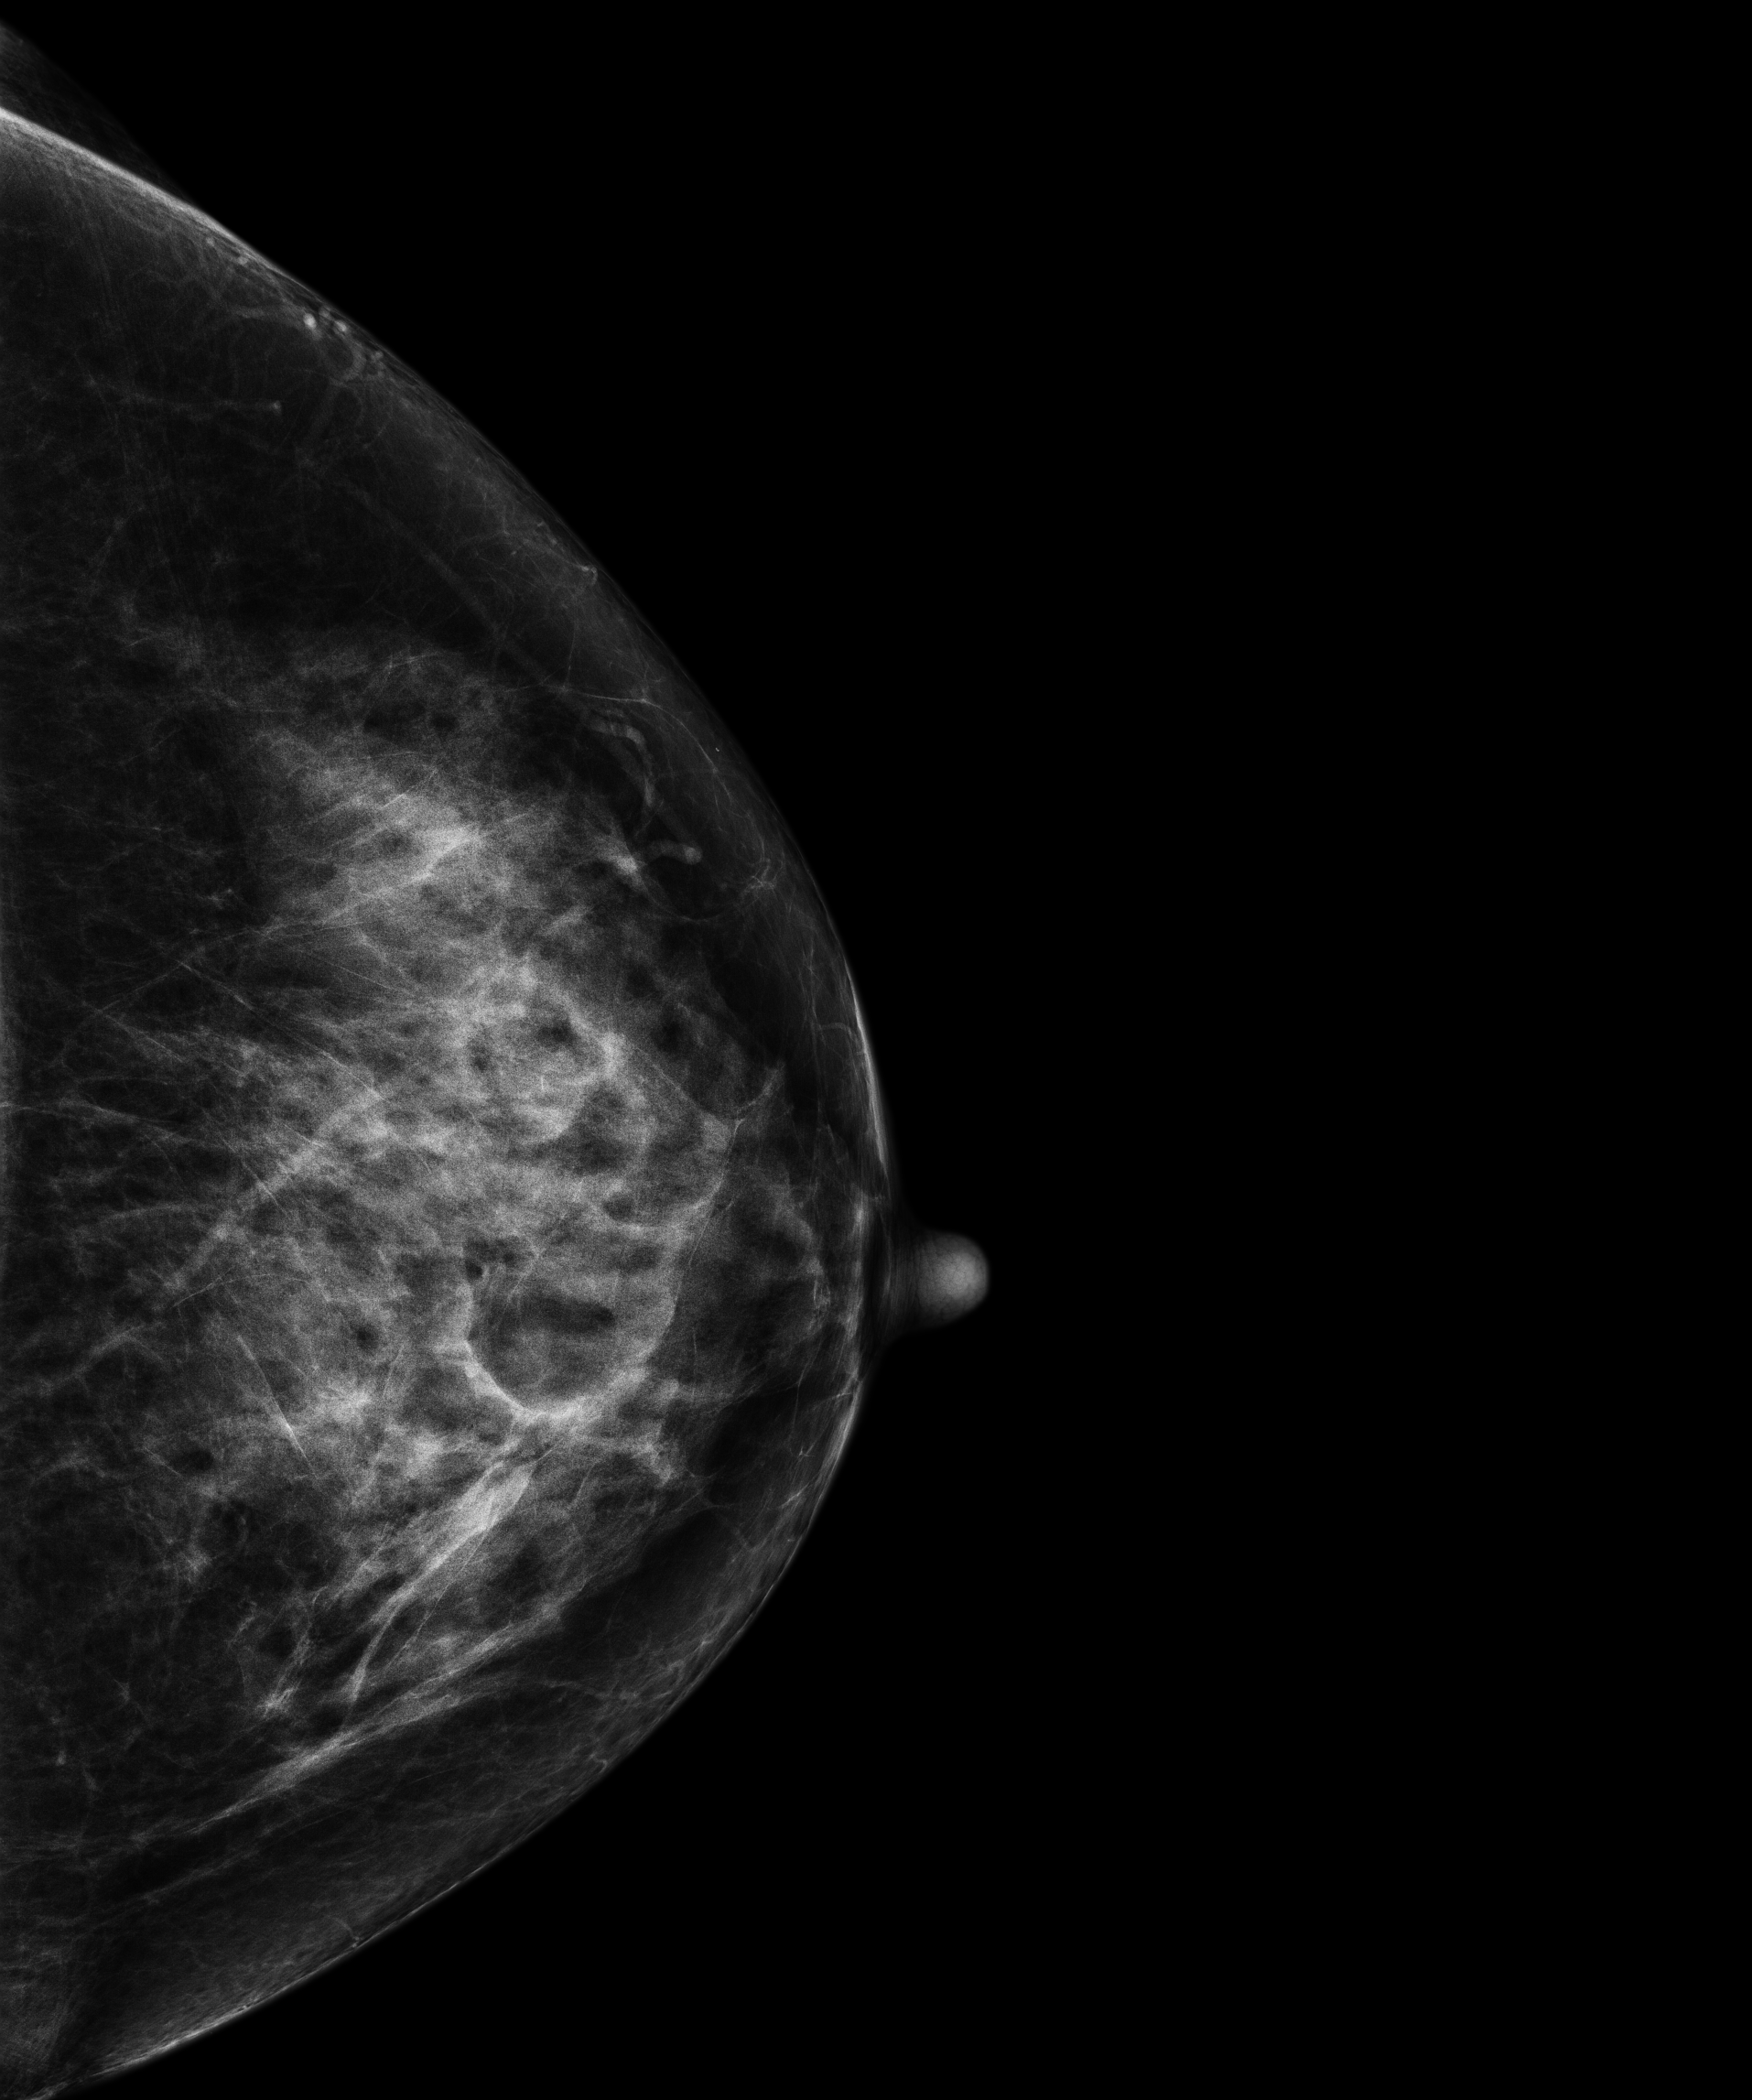
Annual screening mammography examination. Patient aged 68 years (female).
Image type: full-field digital mammogram. Breast: left. Projection: craniocaudal (CC) view.